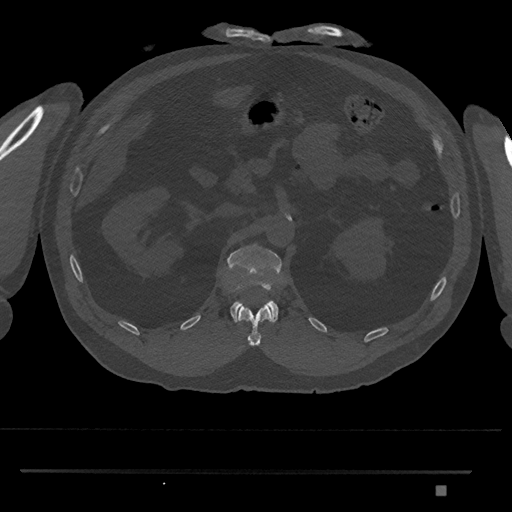
CT including the spine, one axial slice; position 856 of 1134 along the scan axis; reconstruction kernel Br40s/3; bone window (W 1800 / L 400 HU); 0.5 mm slice thickness; 512 × 512 image matrix, field of view 429 × 429 mm. Patient: male, 65 years. From the clinical record (not read from this slice): primary cancer: prostate.
Structures marked on this image (semi-automatic segmentation, software-assisted and operator-edited):
- L1 vertebra: box from (x=226, y=244) to (x=283, y=323) px
- T12 vertebra: (x=237, y=303)–(x=272, y=346)